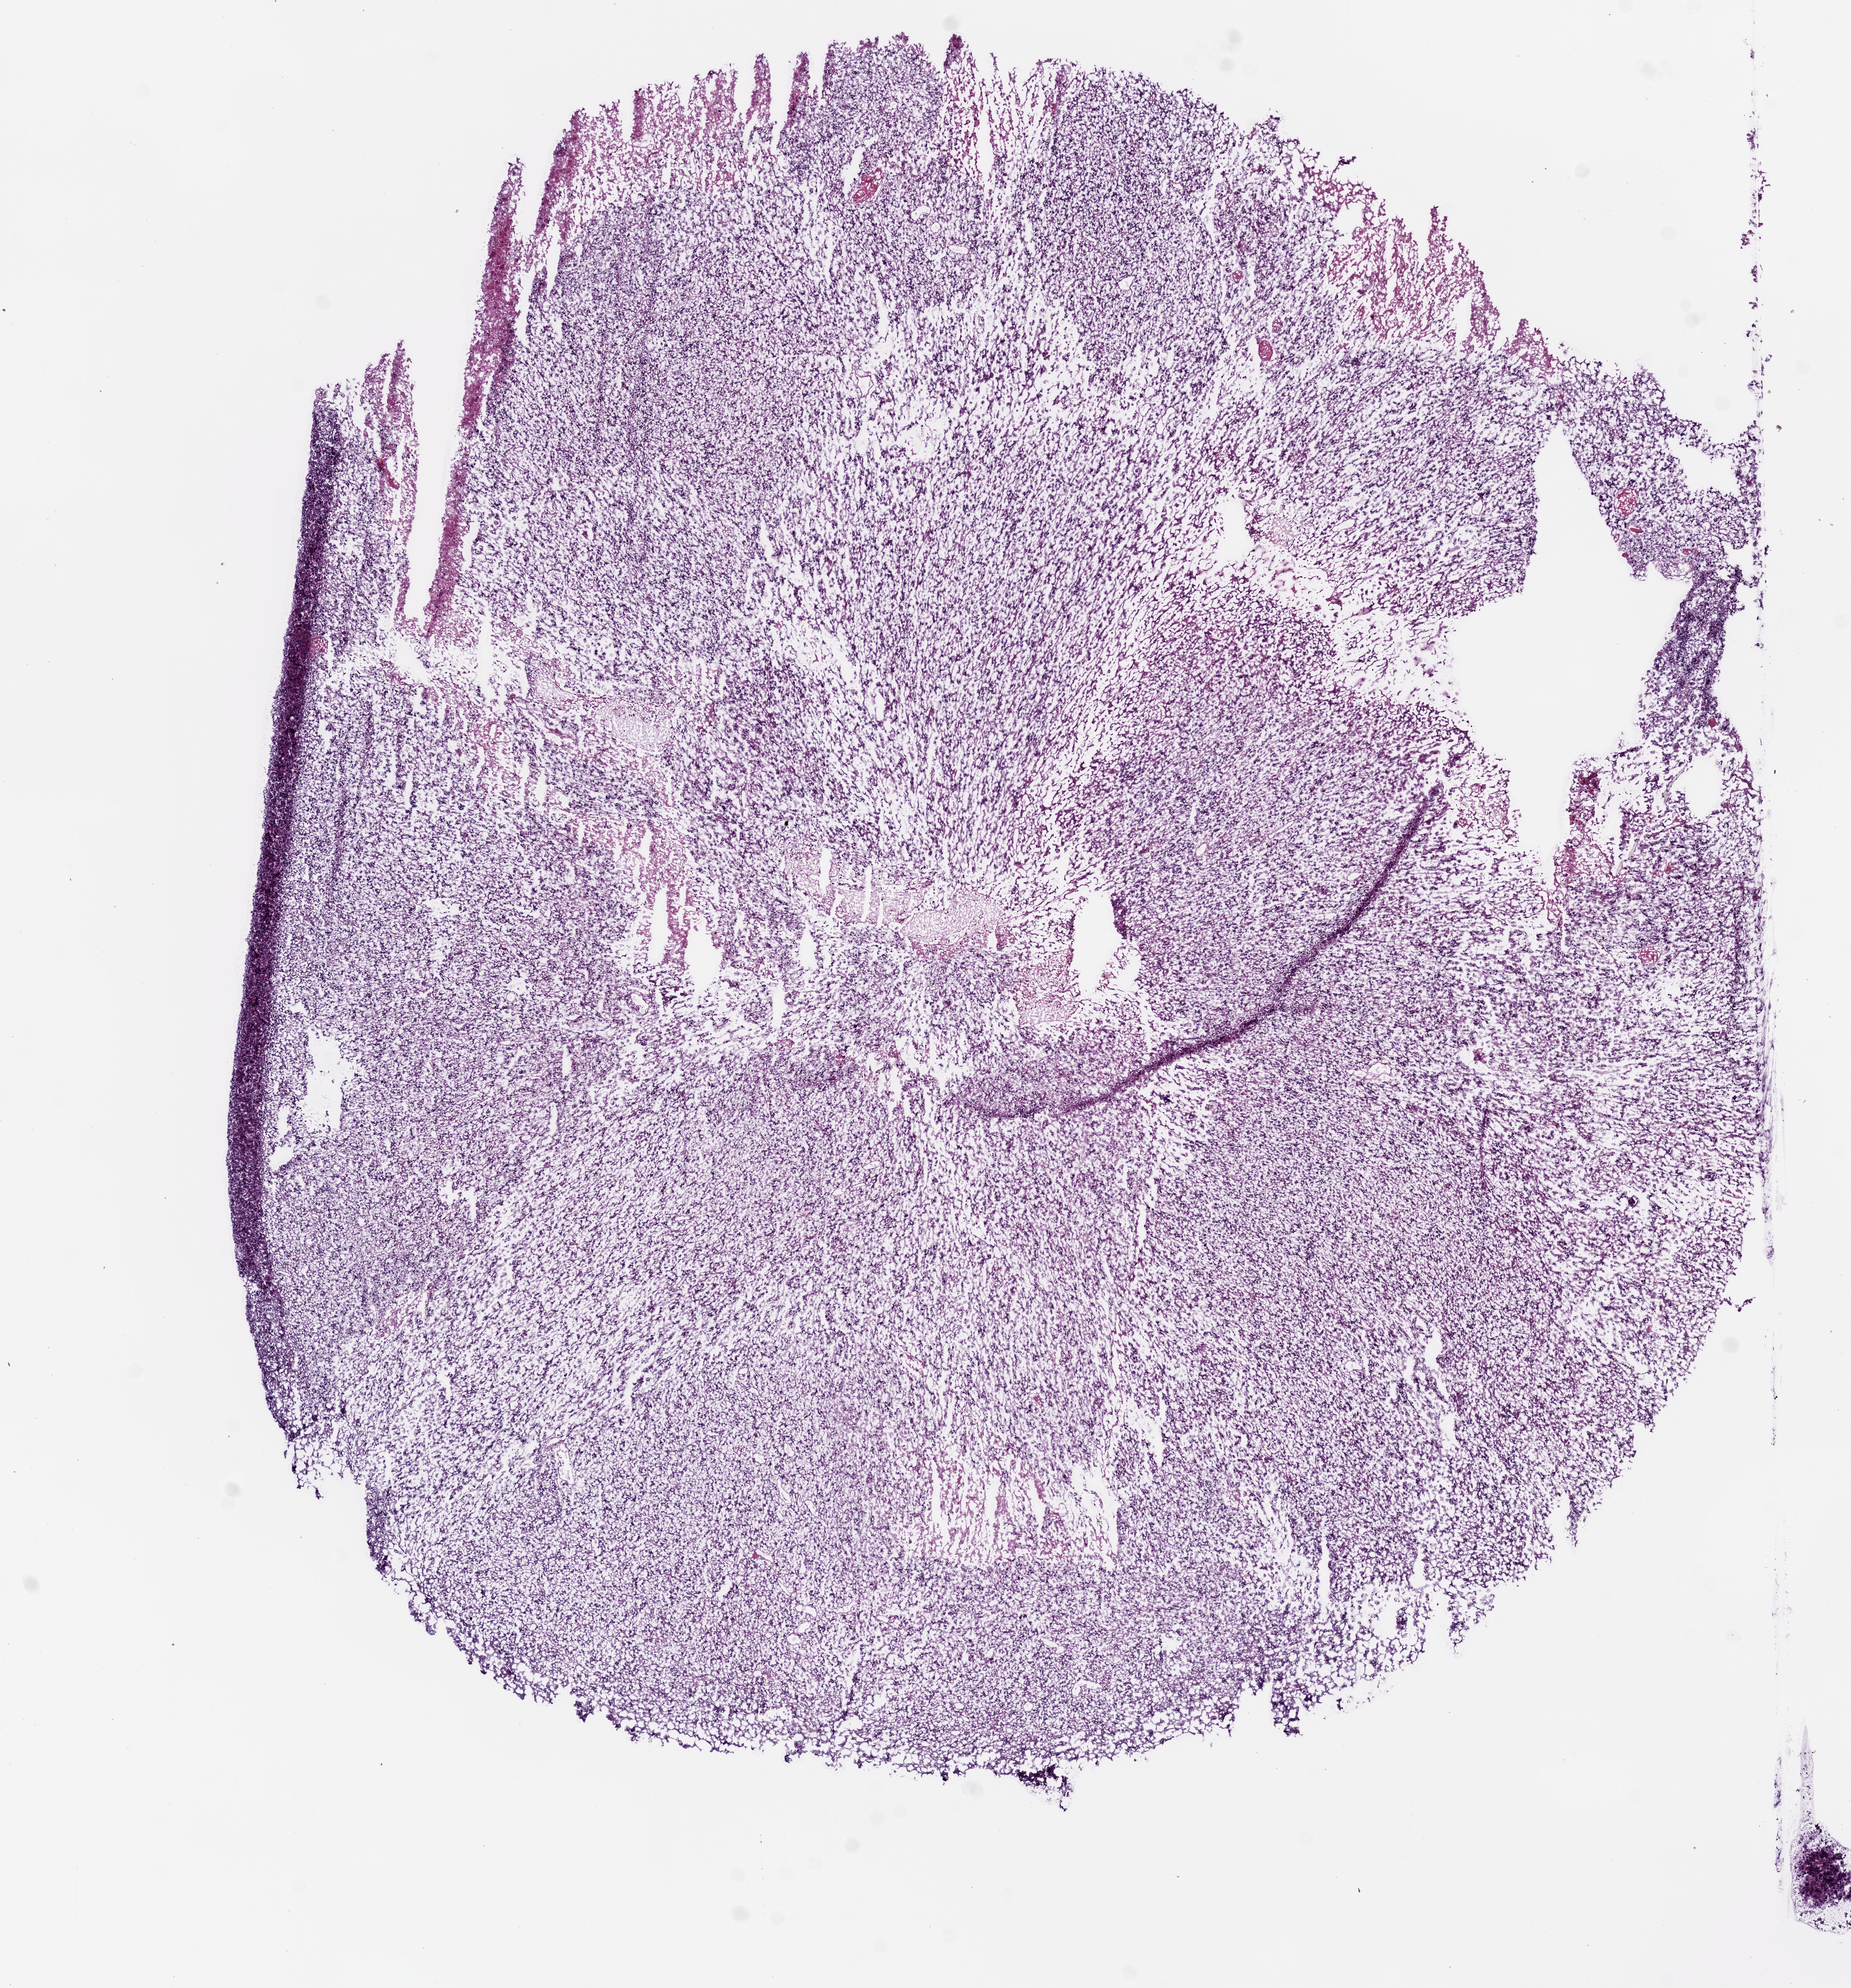
Digitized H&E tissue section (whole slide), the whole scanned area (about 10.3 x 11.1 mm) at the scan's own resolution, acquired at 5x; frozen section; brain, primary tumour sample. Female, age 45 years at initial diagnosis. Composition of this section per pathologist review: tumour cells 95%, tumour nuclei 85%, normal cells 0%, stromal cells 0%, necrosis 5%.
Histologic diagnosis: Glioblastoma.